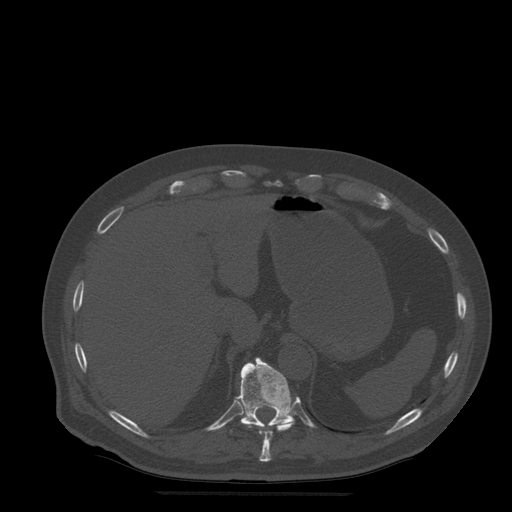
CT including the spine, one axial slice. Position 254 of 522 along the scan axis. Bone window (W 1800 / L 400 HU). 1.25 mm slice thickness. 512 × 512 image matrix. Patient age 72 years. From the clinical record (not read from this slice): primary cancer: prostate.
Annotated regions visible in this slice (semi-automatically segmented with operator editing):
- T10 vertebra: bounding box (x1, y1, x2, y2) in pixels: (241, 422, 294, 462)
- T11 vertebra: (231, 358, 295, 433)